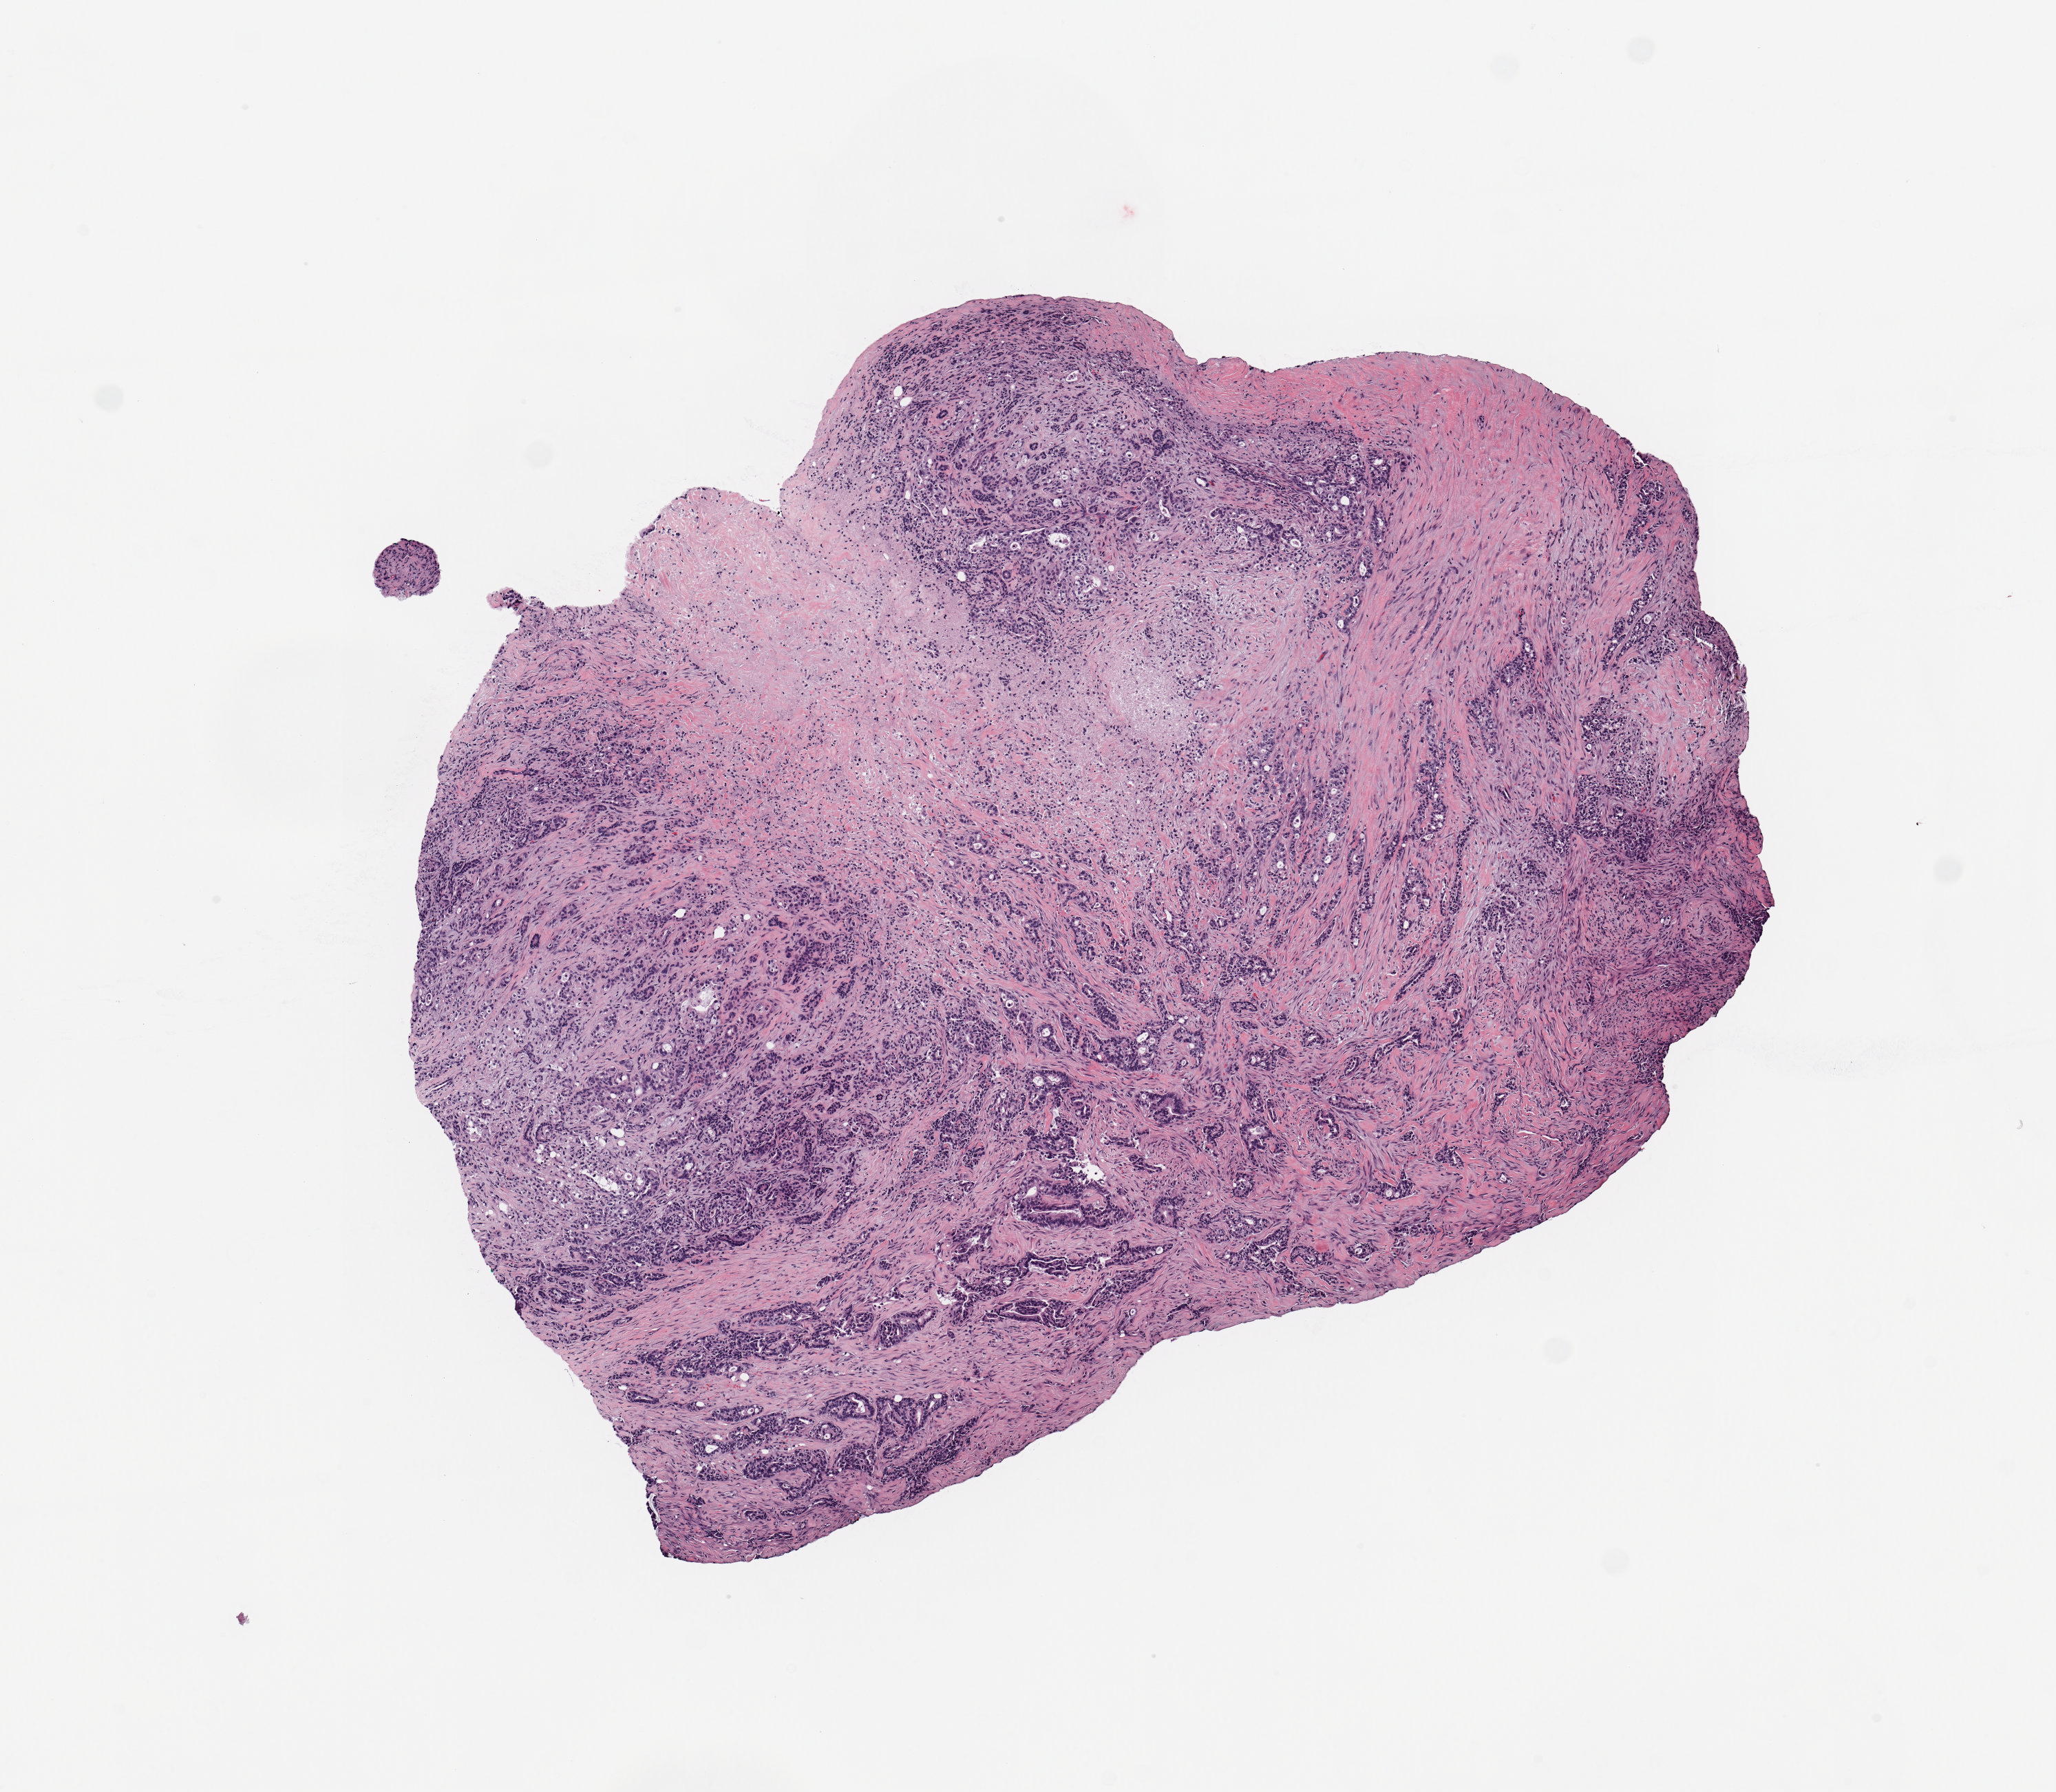
Hematoxylin and eosin (H&E) stained whole-slide image — shown as a low-resolution overview of the whole scanned area (about 5.9 x 5.1 mm, from a 20x scan), tumour tissue sample, sampled site: pancreas. Patient: male, age 70 years.
Diagnosis: Infiltrating duct carcinoma, NOS.